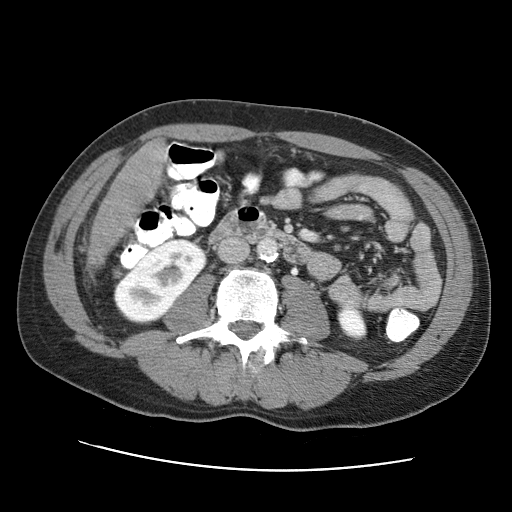
Contrast-enhanced abdominal CT (liver protocol), one axial slice. Slice 10 of 95 in the series (ordered by position). 120 kVp. One of 2 acquisitions stored at this slice position. Soft-tissue window (W 400 / L 40 HU). 512 × 512 image matrix. From the clinical record (not read from this slice): diagnosis: hepatocellular carcinoma (patient treated with transarterial chemoembolisation; whether this scan precedes or follows treatment is not stated here); TNM stage (as recorded): Stage-IVA; Child-Pugh class: A; tumour differentiation: moderately differentiated; tumour nodularity: multinodular.
Annotated regions visible in this slice (semi-automatic segmentation, software-assisted and operator-edited):
- liver parenchyma outside the tumour (the mass and vessels are separate outlines, so this box may not span the whole liver): bounding box (x1, y1, x2, y2) in pixels: (128, 142, 166, 195)
- mass: (85, 158, 154, 268)